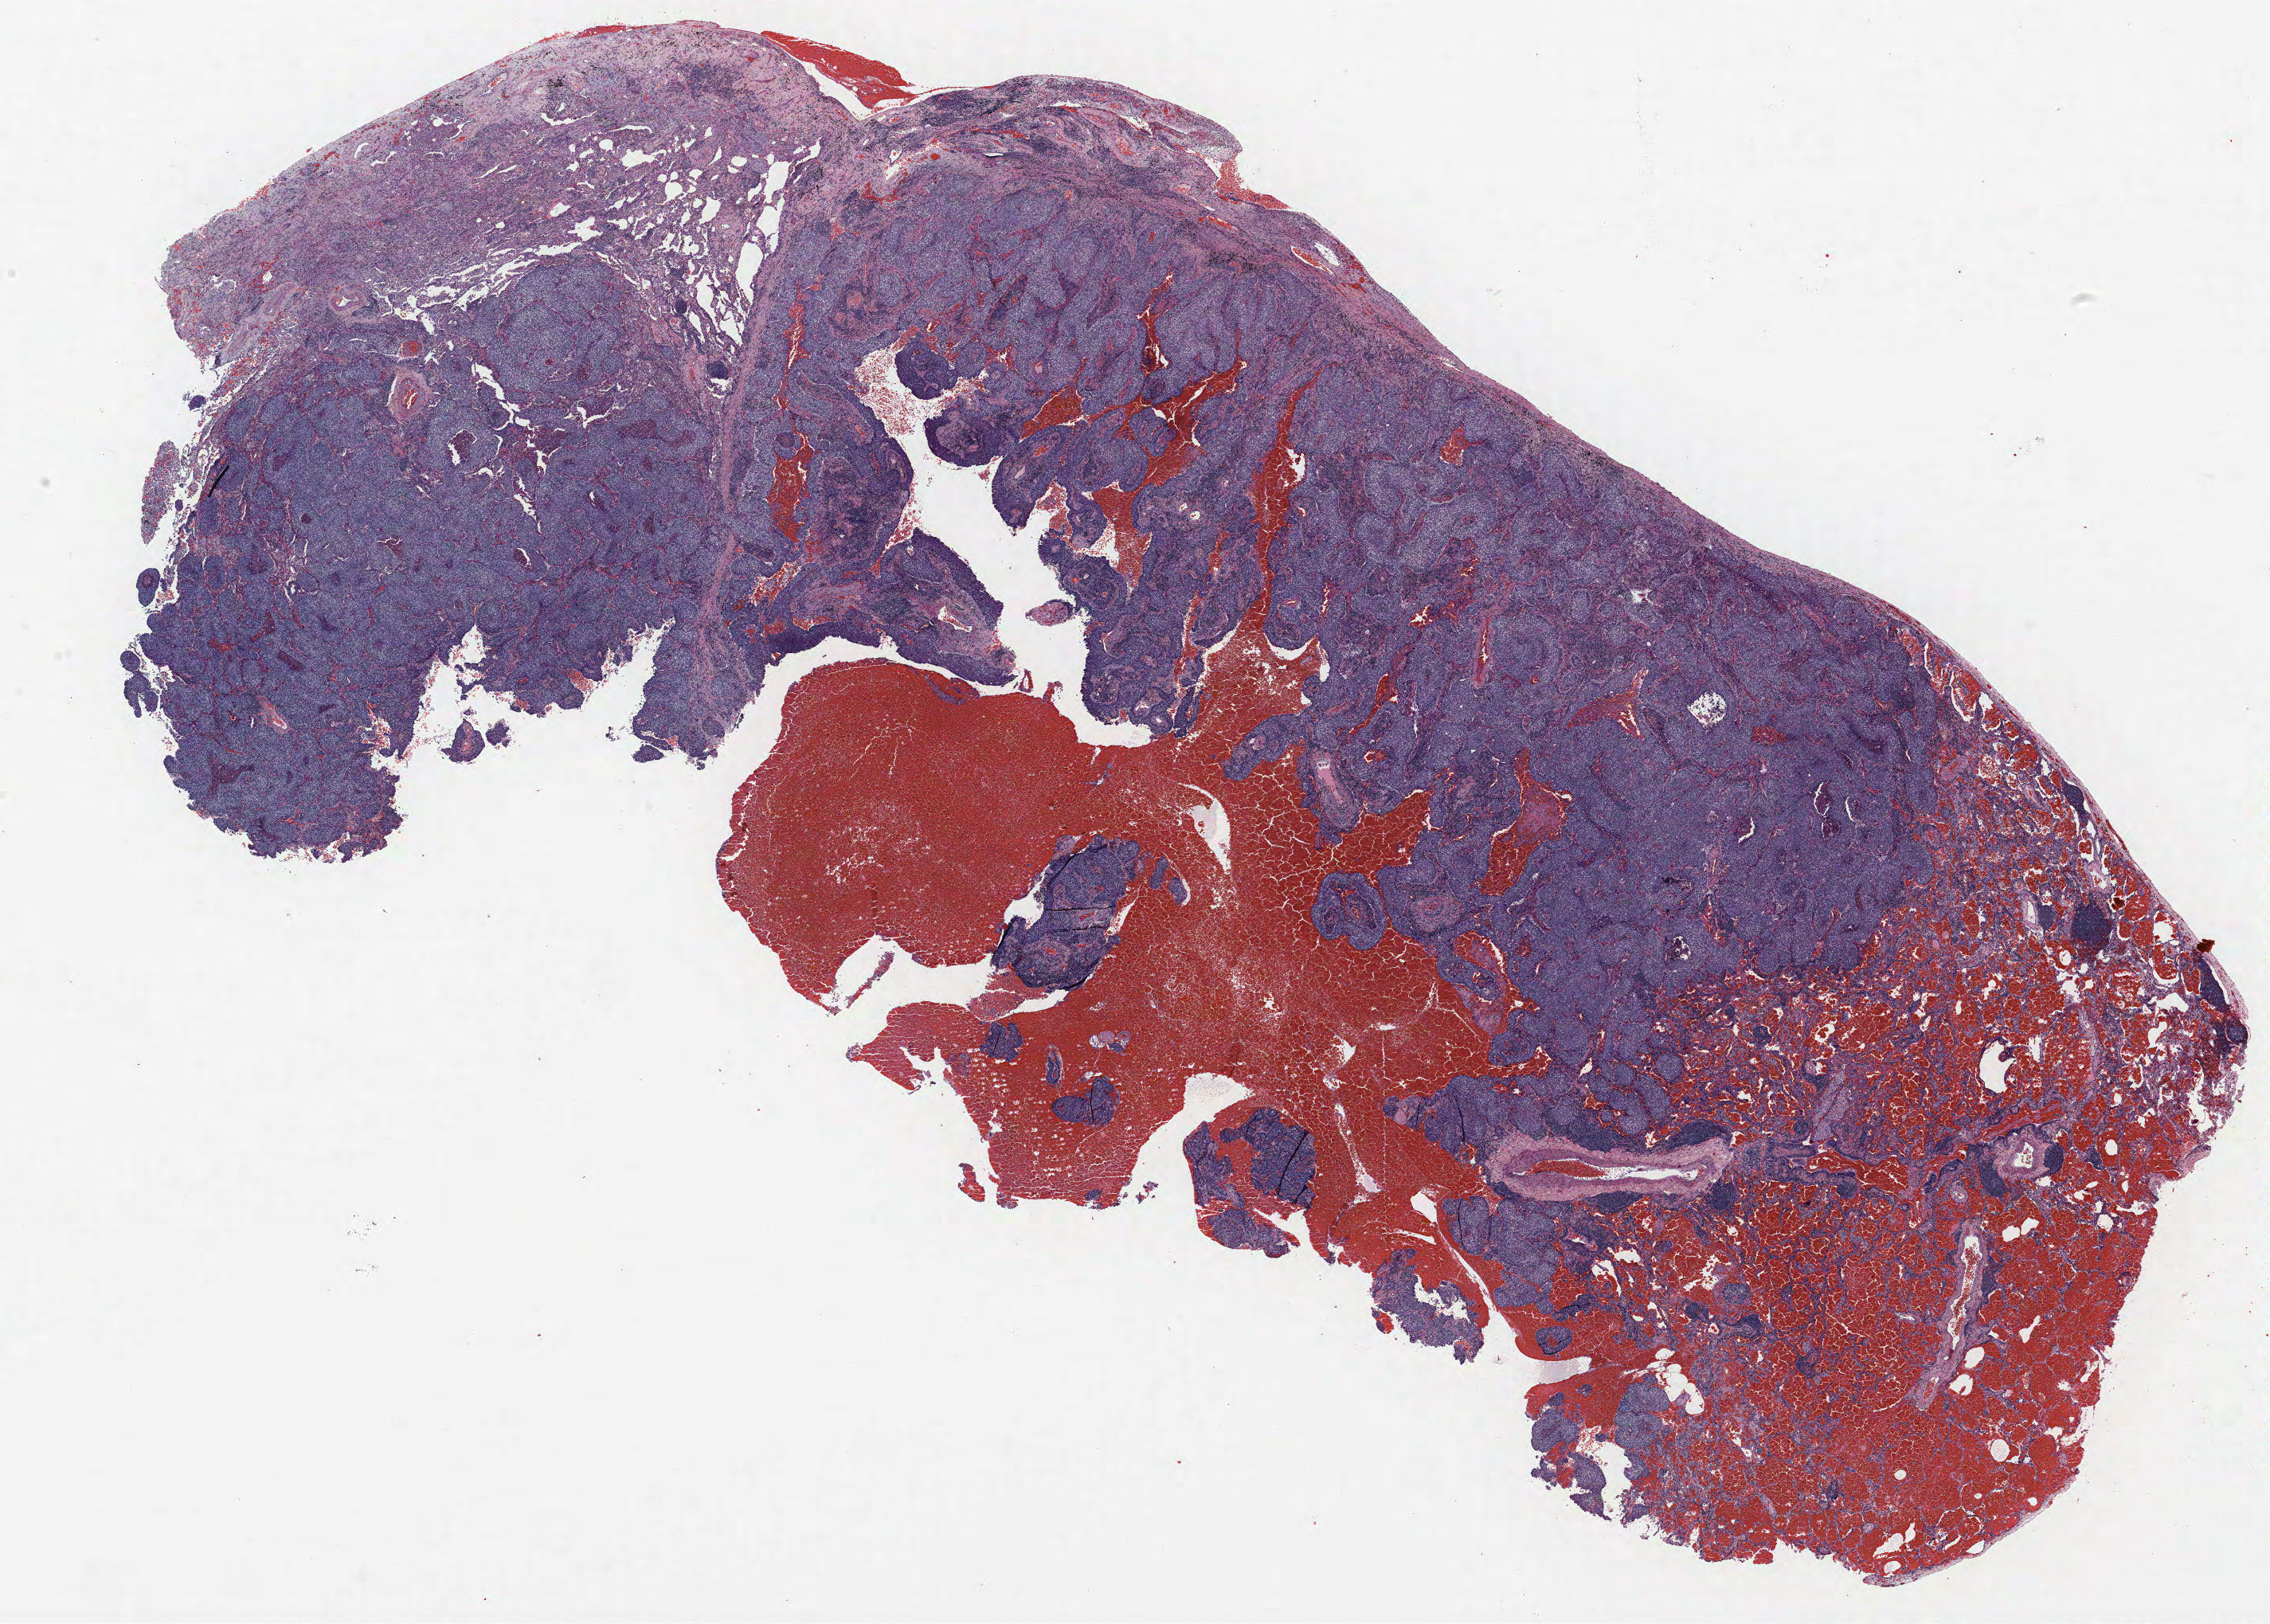
H&E whole-slide image, a low-resolution overview of the entire scanned area, about 22.8 x 16.3 mm, formalin-fixed paraffin-embedded (FFPE) section, lung tissue. Male patient, aged 65 at enrolment. Former smoker at enrolment. Grade: moderately differentiated (G2).
Tumour size (pathology): 25 mm. ICD-O-3 topography: middle lobe of lung (C34.2). Participant's lung-cancer diagnosis: Adenocarcinoma, NOS (ICD-O-3 8140/3). Stage (AJCC 6th edition): IA. Primary tumour location (clinical record): right middle lobe.